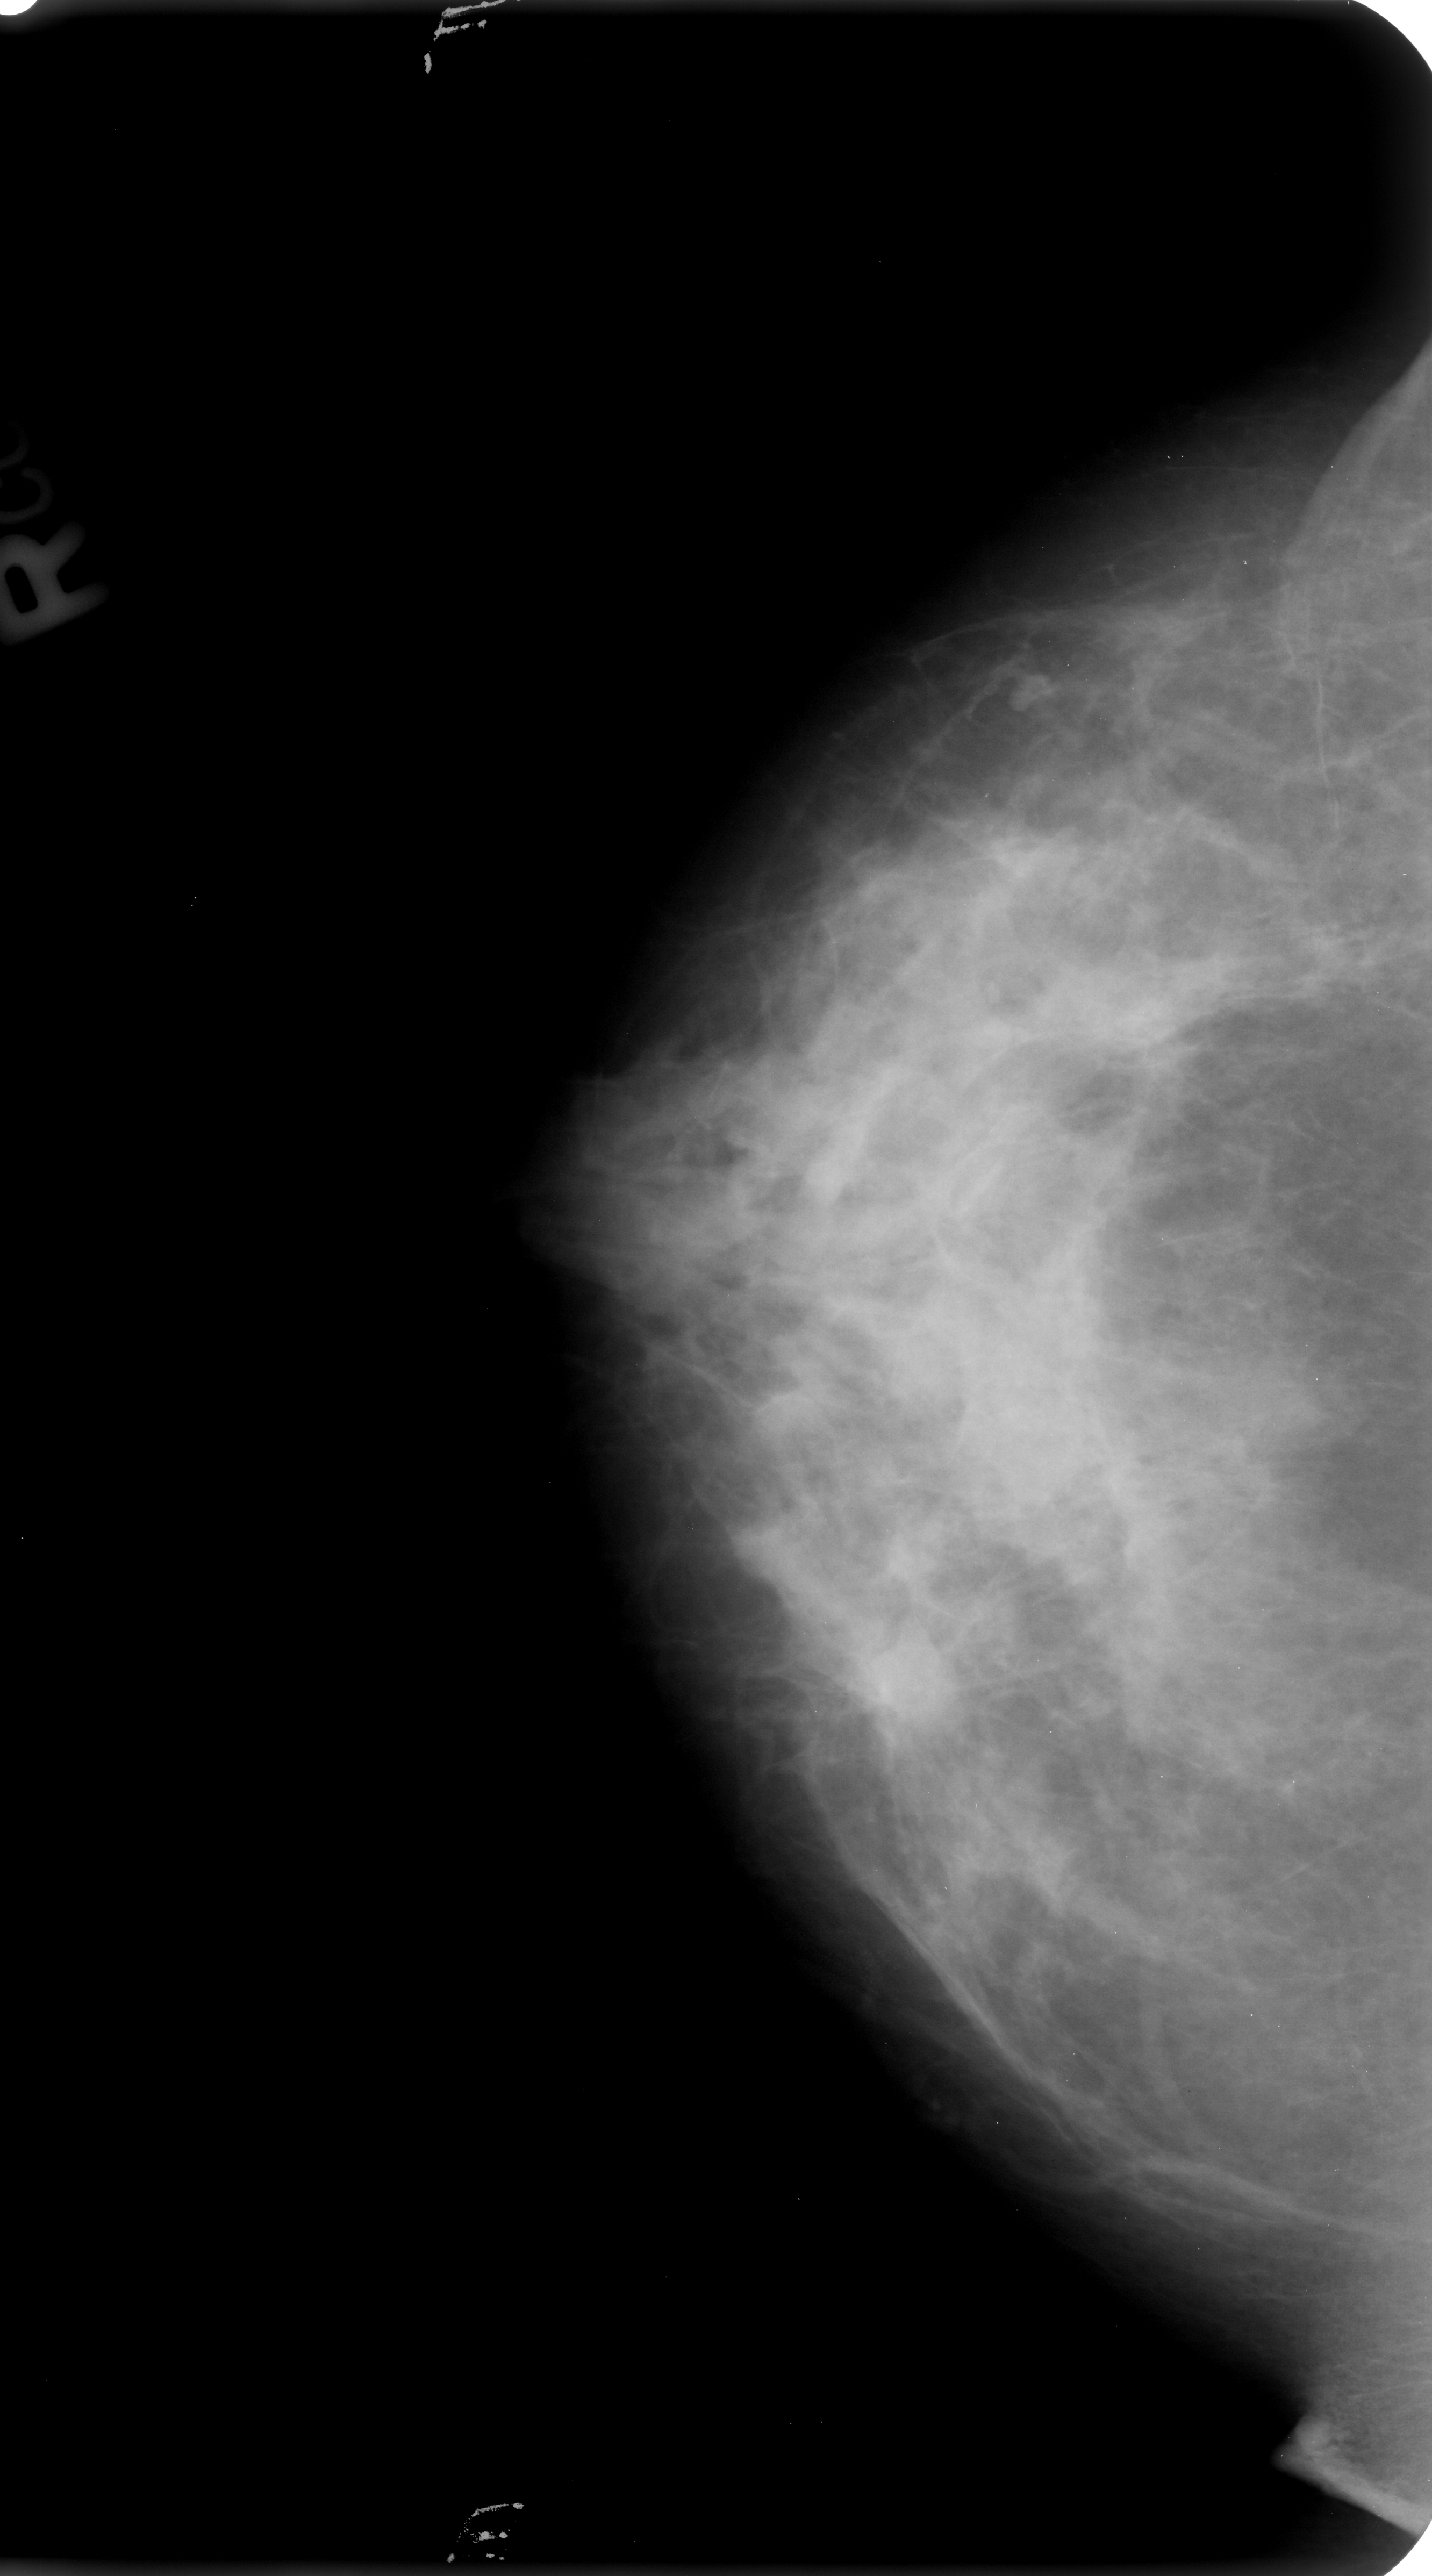
Digitized screen-film mammogram, right breast, craniocaudal (CC) view, BI-RADS breast density category 3 (scale 1–4).
Abnormality record for this image: mass, shape irregular, margins ill defined / spiculated; BI-RADS assessment category 4; subtlety rating 2 on a 1 (subtle) to 5 (obvious) scale; pathology result (as recorded, not read from the image): benign.